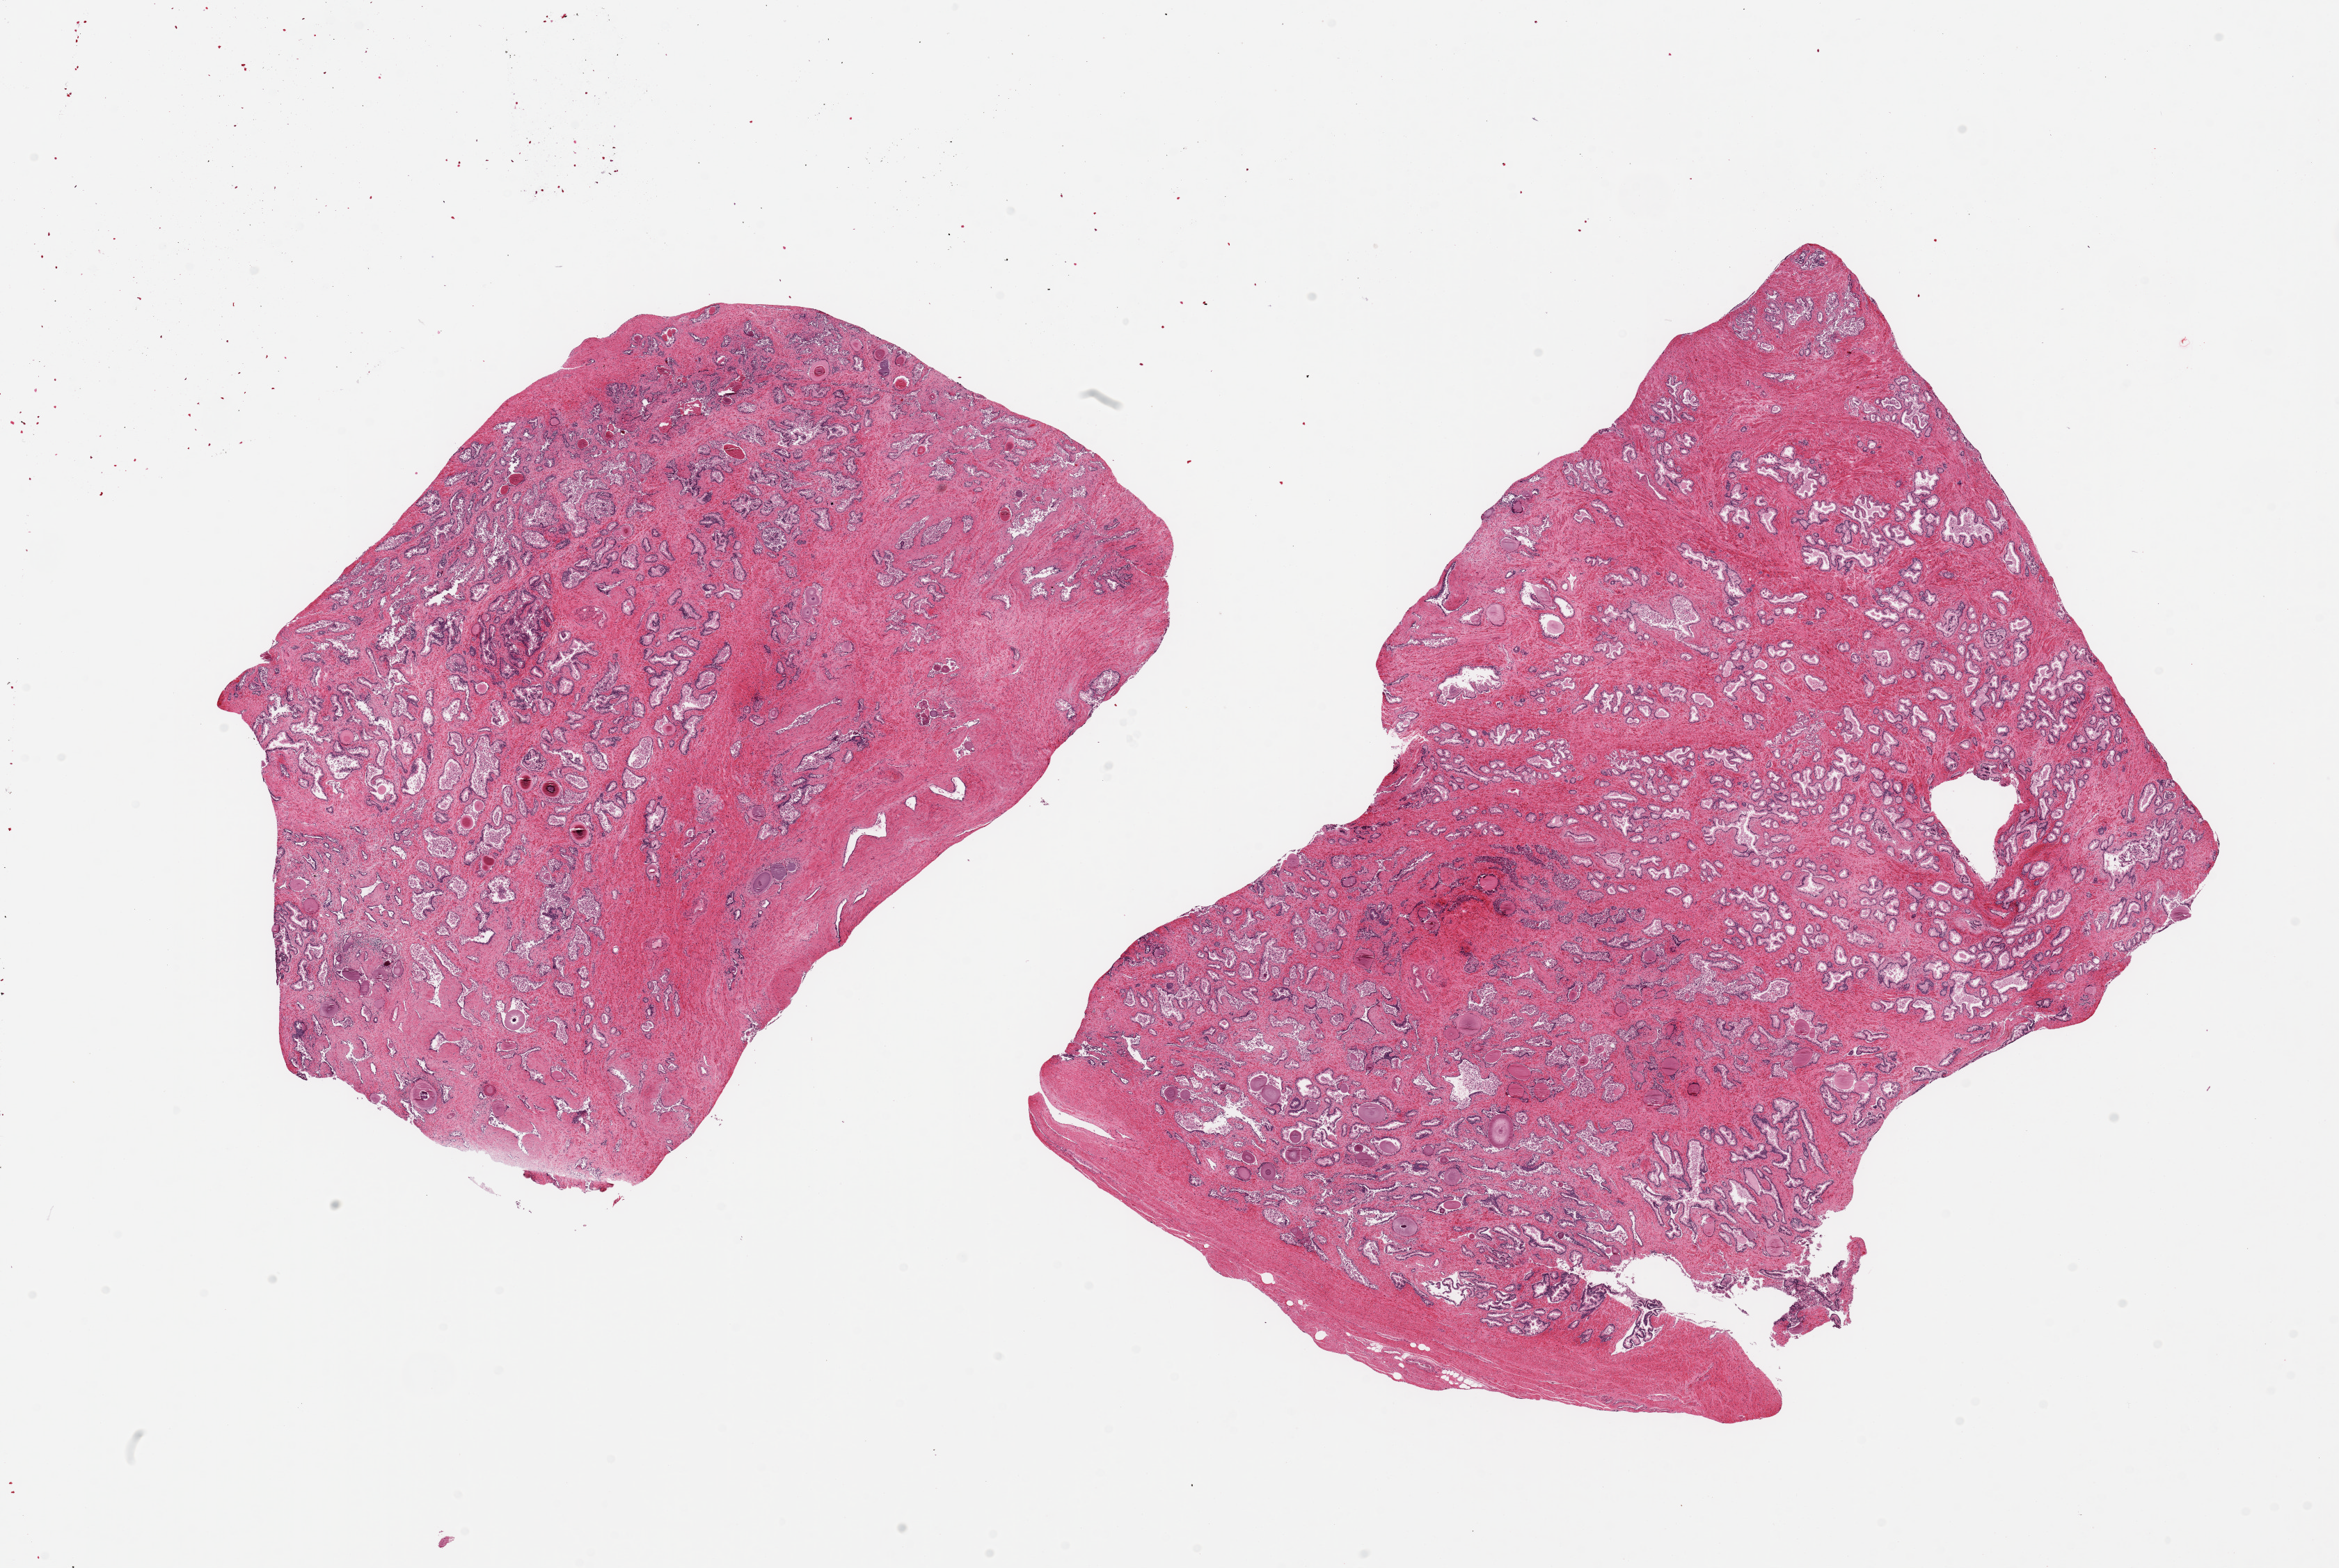
Whole-slide image, hematoxylin and eosin (H&E) stain, a low-resolution overview of the entire scanned area, about 26.6 x 17.8 mm (slide scanned at 20x). PAXgene-fixed paraffin-embedded (PFPE) section. Section of prostate (target tissue). Tissue donor sample. Donor: male.
• pathologist's review note for this sample: 2 pieces; glands evenly distributed